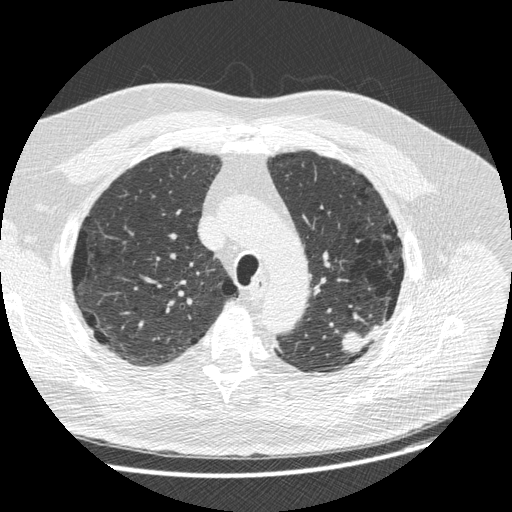
Low-dose screening chest CT, one axial slice; slice 199 of 258 in the series (ordered by position); lung window (W 1500 / L -600 HU); 1.25 mm slice thickness; 512 × 512 image matrix, field of view 370 × 370 mm.
Outlined on this slice (manually delineated by an expert):
- lesion 1 (tumor, upper lobe of left lung): bounding box <342,325,382,354> (left, top, right, bottom; pixels)